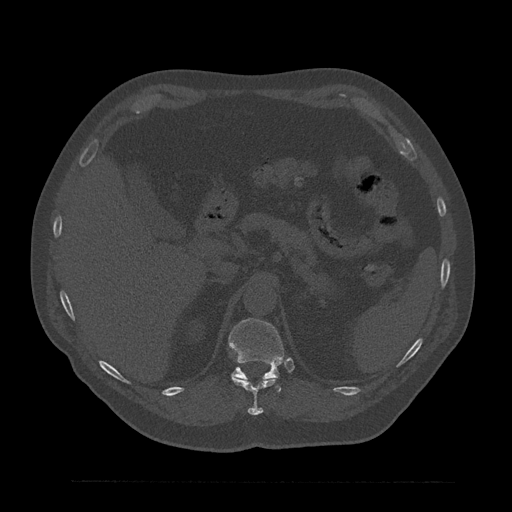
CT including the spine, one axial slice; position 260 of 797 along the scan axis; reconstruction kernel Br40s/3; 120 kVp; bone window (W 1800 / L 400 HU); 0.5 mm slice thickness; 512 × 512 image matrix, field of view 430 × 430 mm. Patient: male, 61 years. From the clinical record (not read from this slice): primary cancer: prostate.
Annotated regions visible in this slice (semi-automatically segmented with operator editing):
- T11 vertebra: bounding box <231,375,277,416> (left, top, right, bottom; pixels)
- T12 vertebra: <229,319,284,392>